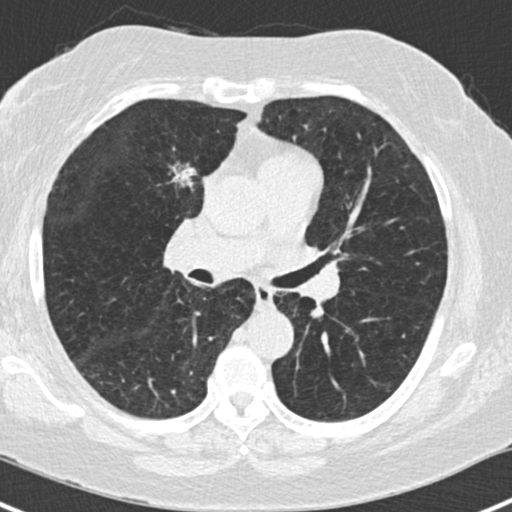
Low-dose screening chest CT, one axial slice. Slice 86 of 168 in the series (ordered by position). Reconstruction kernel B30f. Lung window (W 1500 / L -600 HU). 512 × 512 image matrix, field of view 303 × 303 mm.
Outlined on this slice (expert manual segmentation):
- lesion 1 (tumor, upper lobe of right lung): bounding box [x1, y1, x2, y2] px = [172, 164, 196, 187]